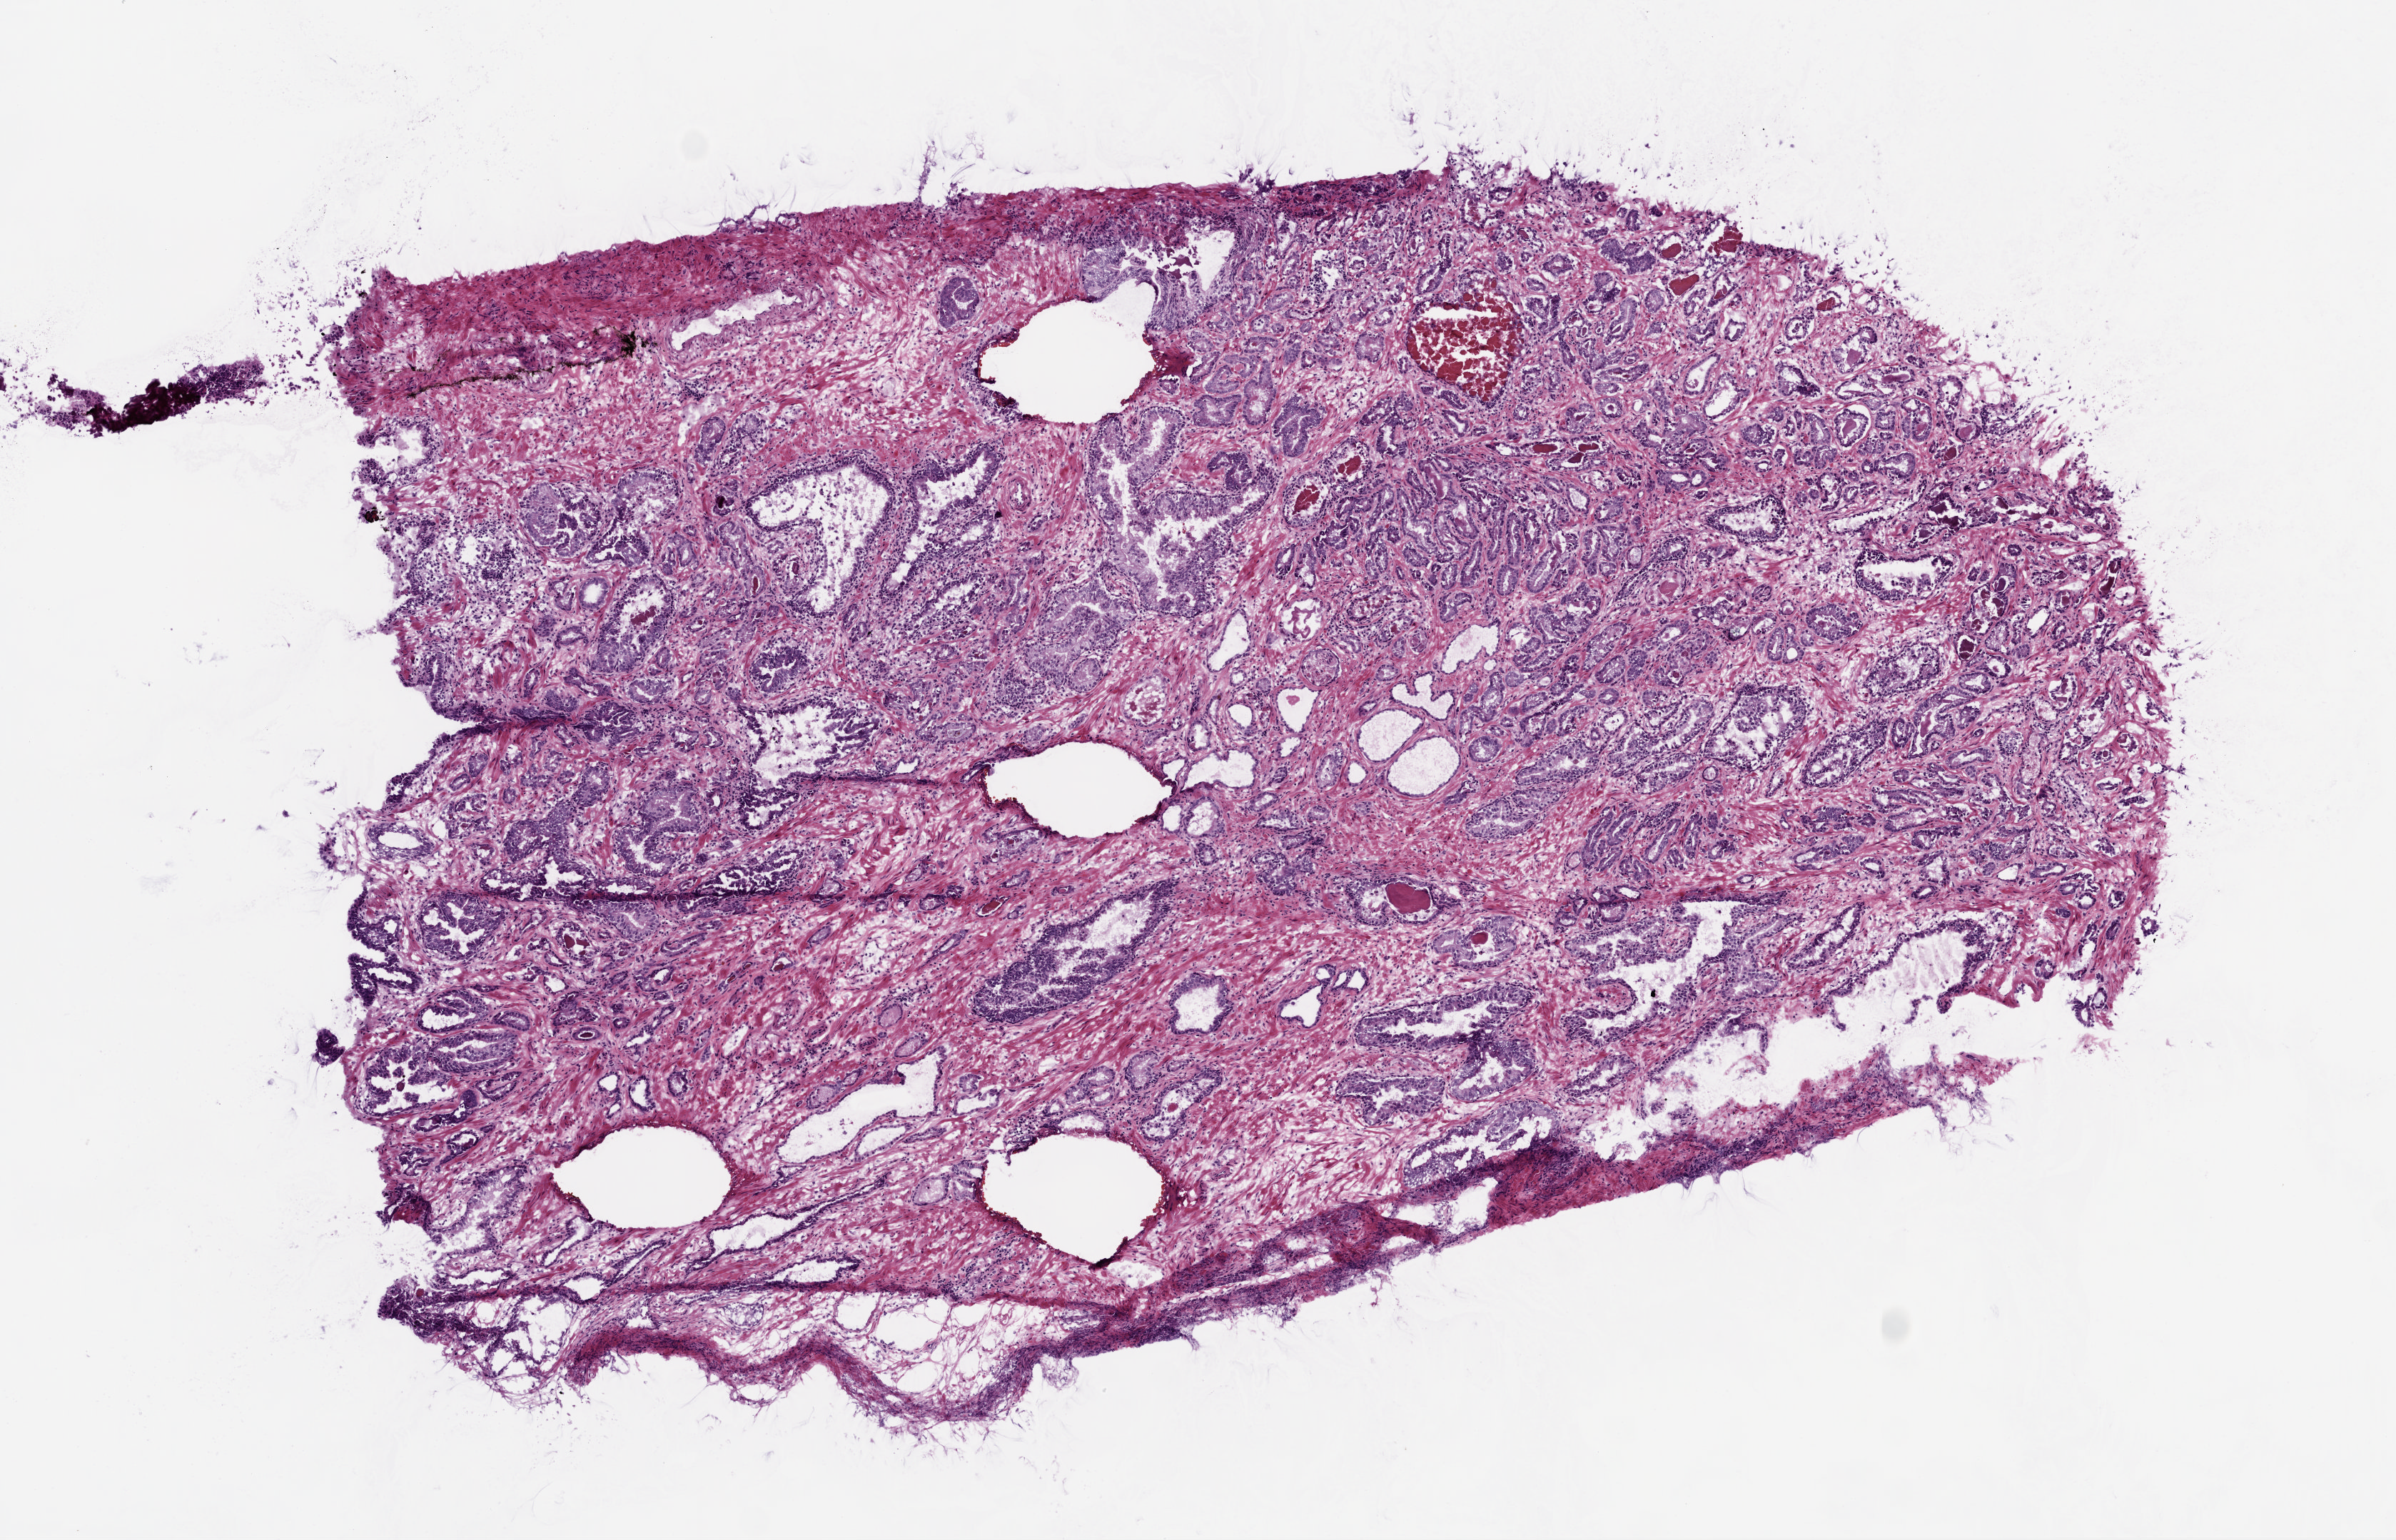
H&E-stained whole-slide image, shown as a low-resolution overview of the whole scanned area (about 6.8 x 4.4 mm); frozen section from the top of the tissue portion; sample: primary tumour, prostate. Male patient; age at initial diagnosis 66 years. Gleason score: 7 (3+4). Composition of this section per pathologist review: tumour cells 70%, tumour nuclei 70%, normal cells 20%, stromal cells 10%, necrosis 0%.
Pathologic diagnosis: Acinar cell carcinoma (prostate gland). Lymph nodes positive (case pathology): 0 of 6 examined. Laterality: bilateral.